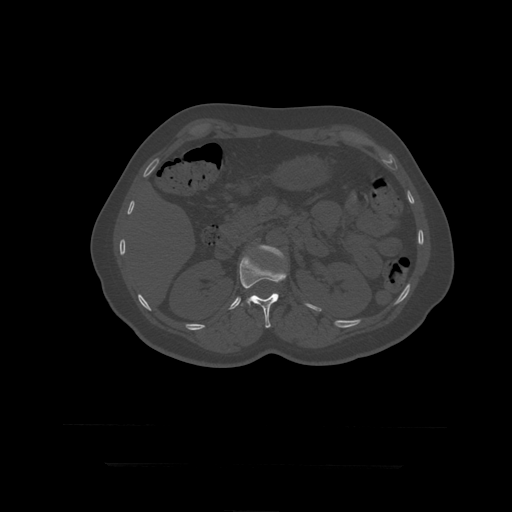
CT including the spine, one axial slice. Position 169 of 399 along the scan axis. Reconstruction kernel STANDARD. 120 kVp. Bone window (W 1800 / L 400 HU). 1.25 mm slice thickness. 512 × 512 image matrix, field of view 450 × 450 mm. Patient age 41 years. From the clinical record (not read from this slice): primary cancer: breast.
Outlined on this slice (semi-automatically segmented with operator editing):
- L1 vertebra: box from (x=240, y=255) to (x=287, y=328) px
- L2 vertebra: (x=259, y=245)–(x=284, y=259)